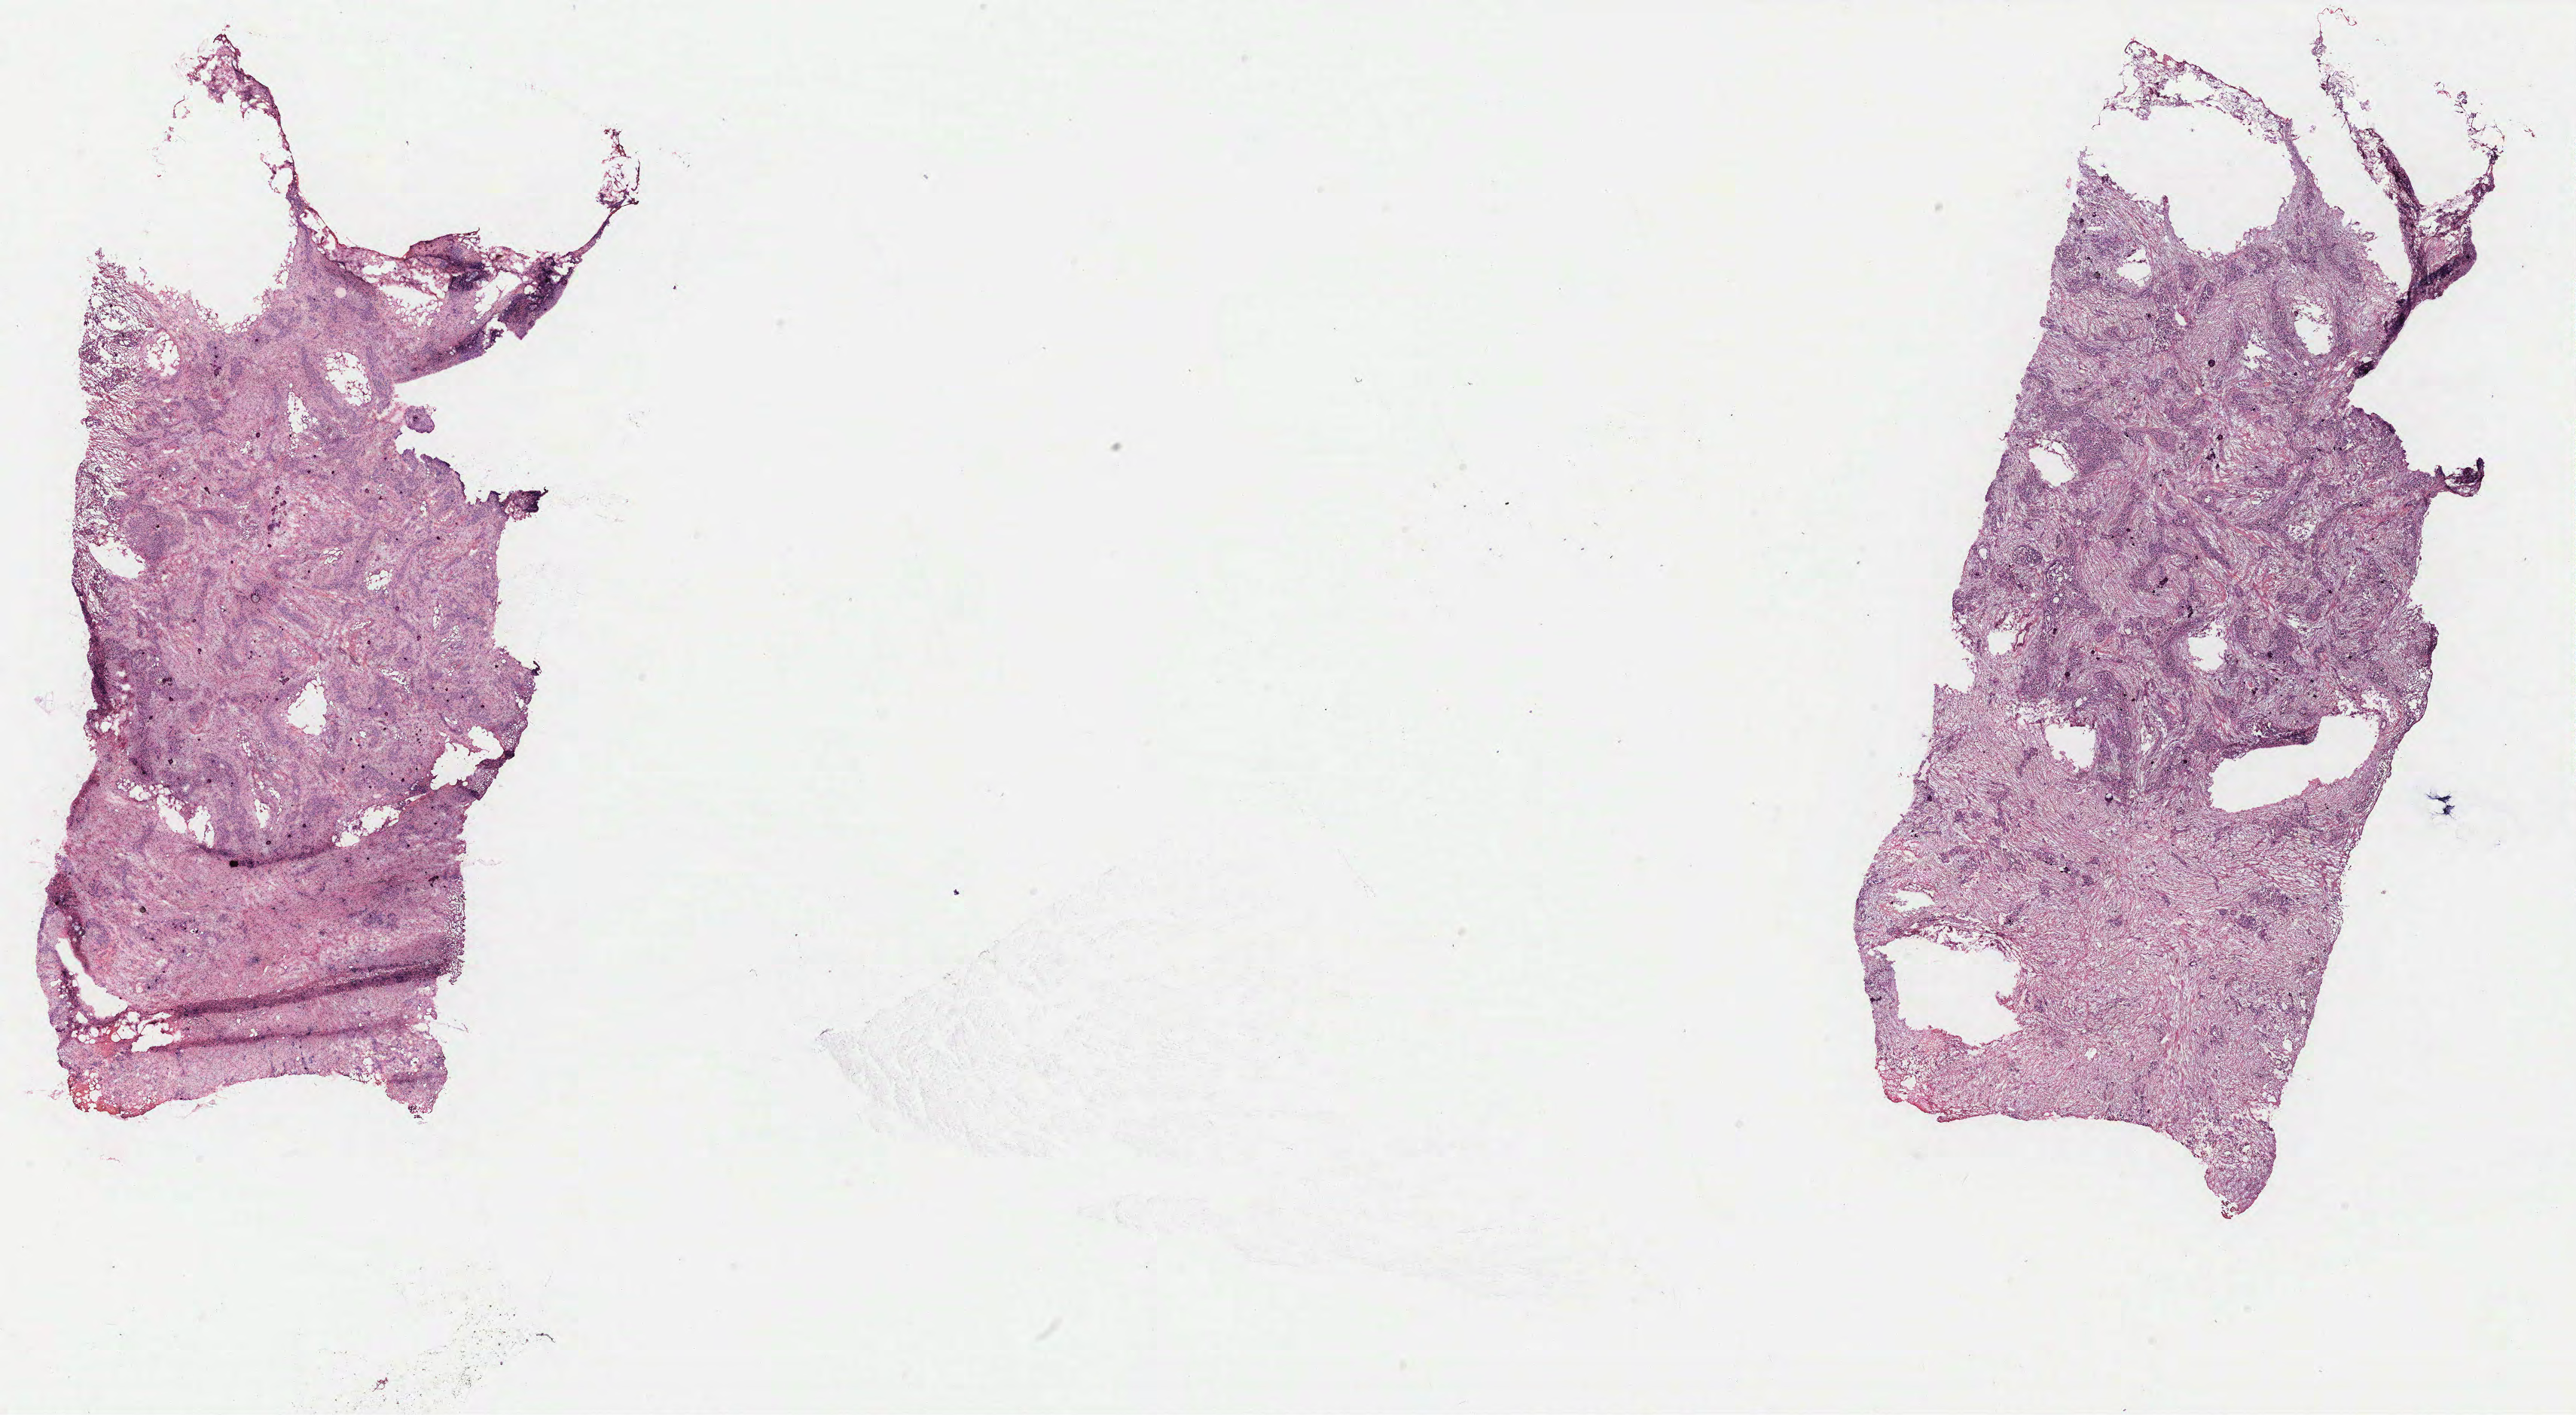
Whole-slide histology image, Hematoxylin and eosin (H&E) stained, shown as a low-resolution overview of the whole scanned area (about 27.4 x 15.0 mm, slide scanned at 40x). Ovary, tumour tissue. 68-year-old female patient.
Primary tumour site (as recorded): peritoneum. Diagnosis: Serous adenocarcinoma, NOS (peritoneum, NOS).